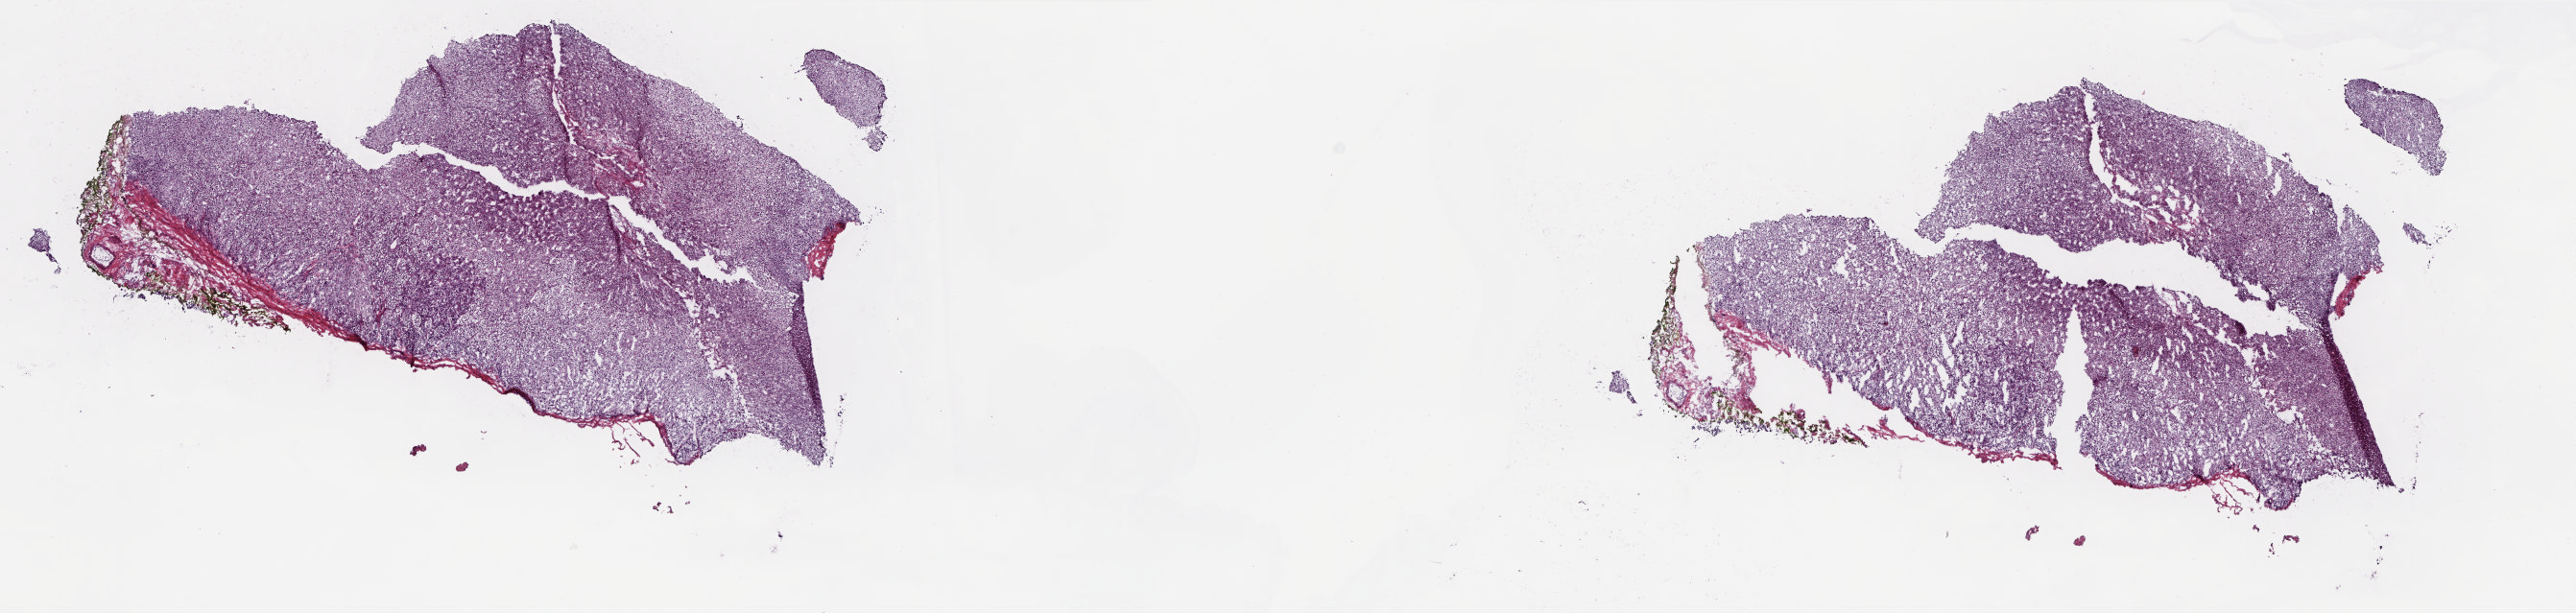
Whole-slide histology image, H&E, low-resolution overview of the scanned area, about 21.6 x 5.2 mm, frozen section, adrenal gland, solid tissue normal (non-tumour tissue) sample. Female, age 35 years at initial diagnosis.
This section: solid tissue normal (non-tumour) sample from the same patient. Patient diagnosis: Pheochromocytoma, NOS.